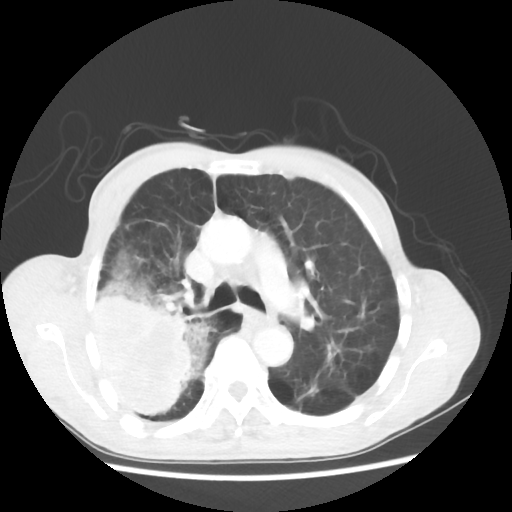
Chest CT, one axial slice; slice 36 of 58 in the series (ordered by position); reconstruction kernel STANDARD; lung window (W 1500 / L -600 HU); 5 mm slice thickness; 512 × 512 image matrix. Patient: male, 75 years. Case-level facts recorded for this patient, not image findings: clinical TNM (as recorded): T4 N1 M1.
Annotated regions visible in this slice (rectangle marked by the reading radiologist):
- lung tumour (recorded histology: adenocarcinoma): box from (x=87, y=262) to (x=209, y=418) px